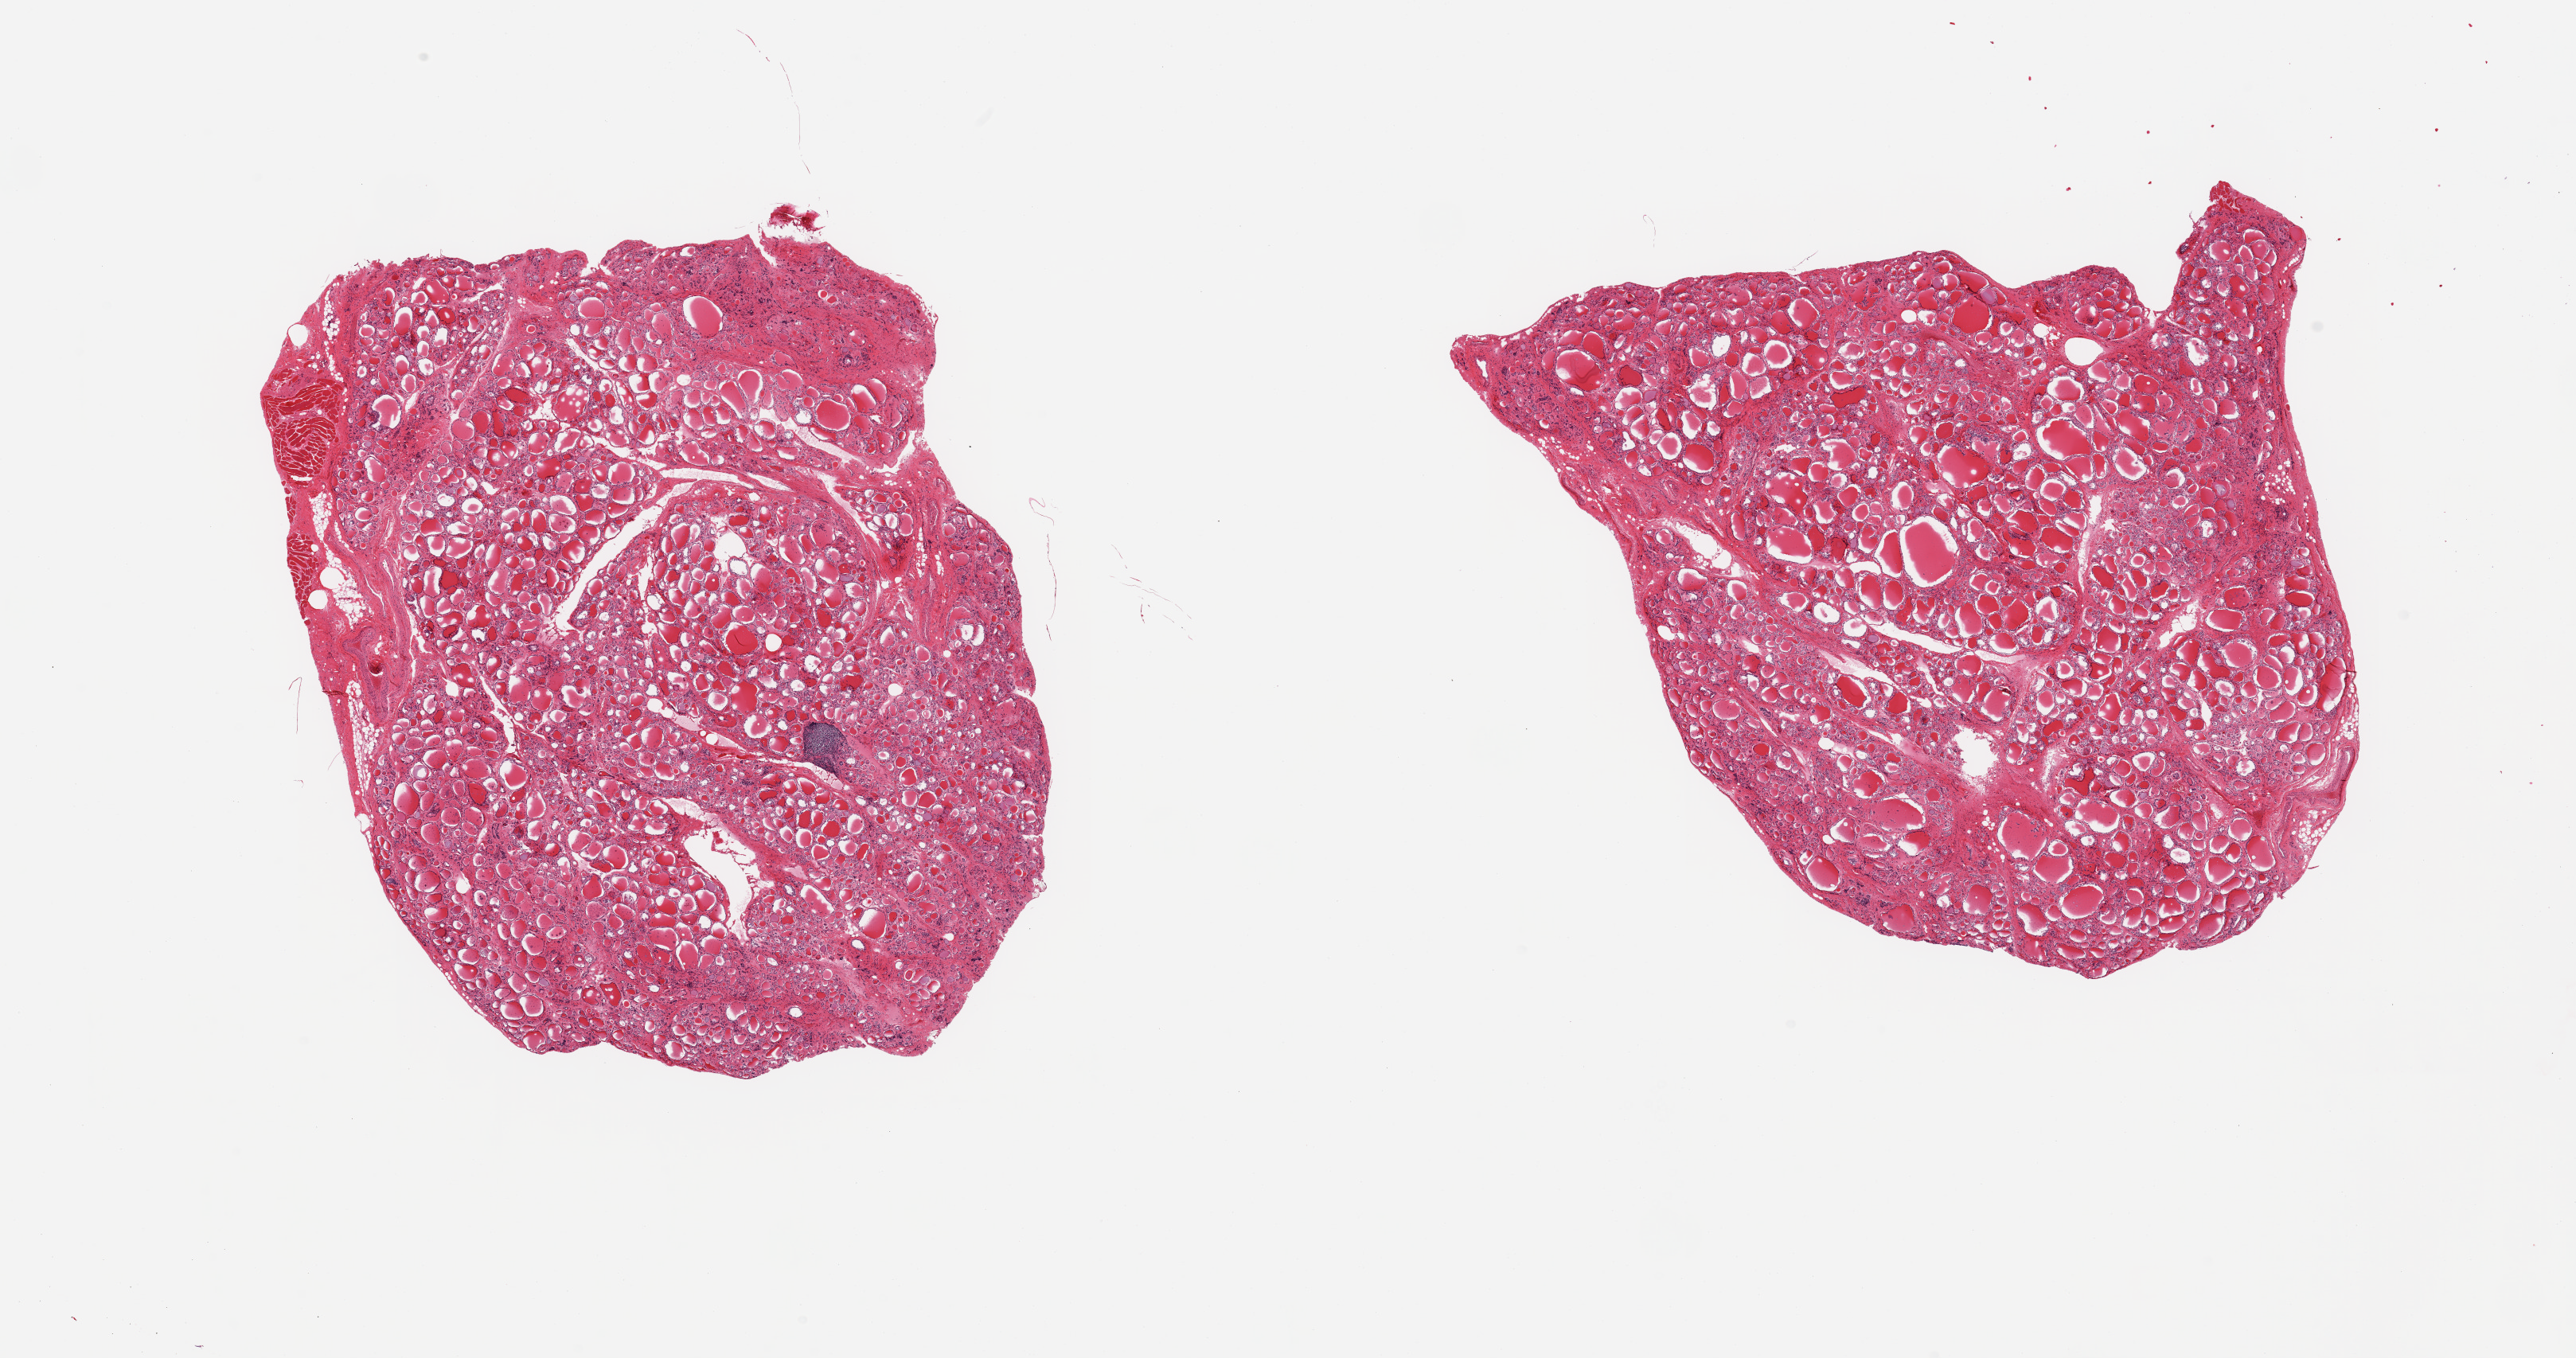
Digitized H&E-stained section, shown as a low-resolution overview of the whole scanned area (about 25.6 x 13.5 mm, slide scanned at 20x), PAXgene-fixed, paraffin-embedded tissue, target tissue: thyroid, donor tissue sample. Donor sex: male.
* review note (as recorded): 2 pieces; focus of atrophy & fibrosis